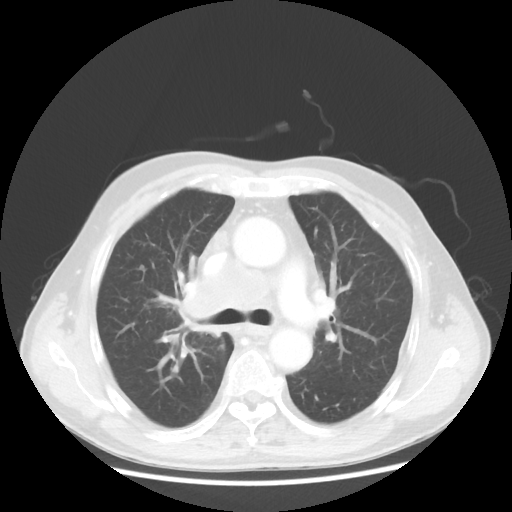
Chest CT, one axial slice; position 77 of 124 along the scan axis; reconstruction kernel STANDARD; 100 kVp; lung window (W 1500 / L -600 HU); 5 mm slice thickness; 512 × 512 image matrix. Patient: male, 64 years. Case-level facts recorded for this patient, not image findings: clinical TNM (as recorded): T3 N3 M0.
Annotated regions visible in this slice (bounding box drawn by a radiologist):
- lung tumour (recorded histology: small cell carcinoma): bounding box [x1, y1, x2, y2] px = [177, 283, 227, 342]